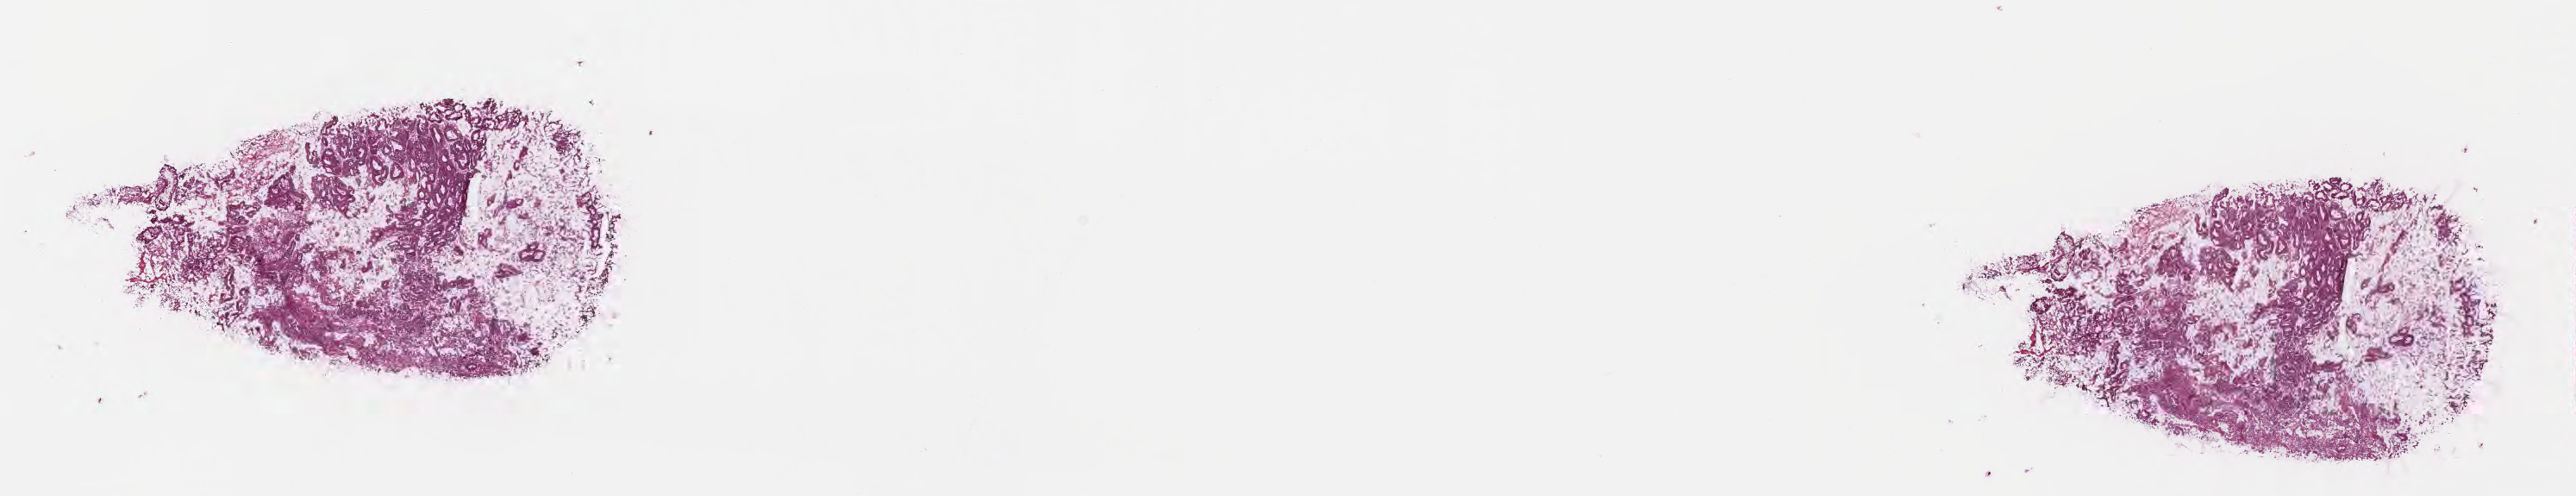
H&E whole-slide image, a low-resolution overview of the entire scanned area, about 24.1 x 4.6 mm. Frozen section. Primary tumor. Site: rectum. Male, age 54 years at initial diagnosis. Tumor grade: G2 (moderately differentiated). Composition of this section per pathologist review: tumor cells 65%, tumor nuclei 65%, stromal cells 20%, necrosis 0%, normal cells 15%. Inflammatory infiltration, as recorded: lymphocyte infiltration 4%, monocyte infiltration 2%, neutrophil infiltration 6%.
Histologic diagnosis: Adenocarcinoma, NOS. AJCC pathologic stage: Stage IIA.